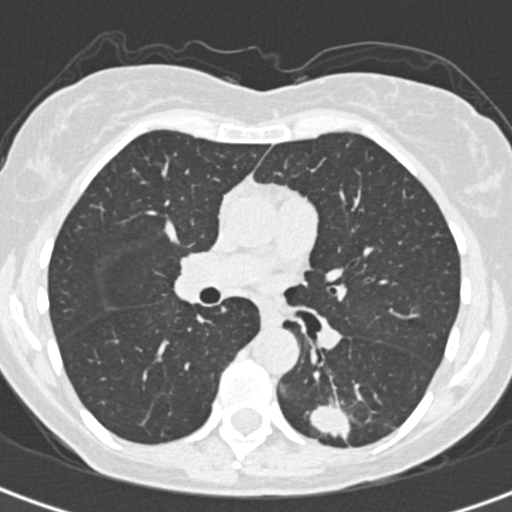
Low-dose screening chest CT, one axial slice. Position 192 of 328 along the scan axis. Reconstruction kernel B30f. Lung window (W 1500 / L -600 HU). 1 mm slice thickness. 512 × 512 image matrix, field of view 284 × 284 mm.
Outlined on this slice (expert manual segmentation):
- lesion 1 (tumor, lower lobe of left lung): bounding box <310,401,351,439> (left, top, right, bottom; pixels)